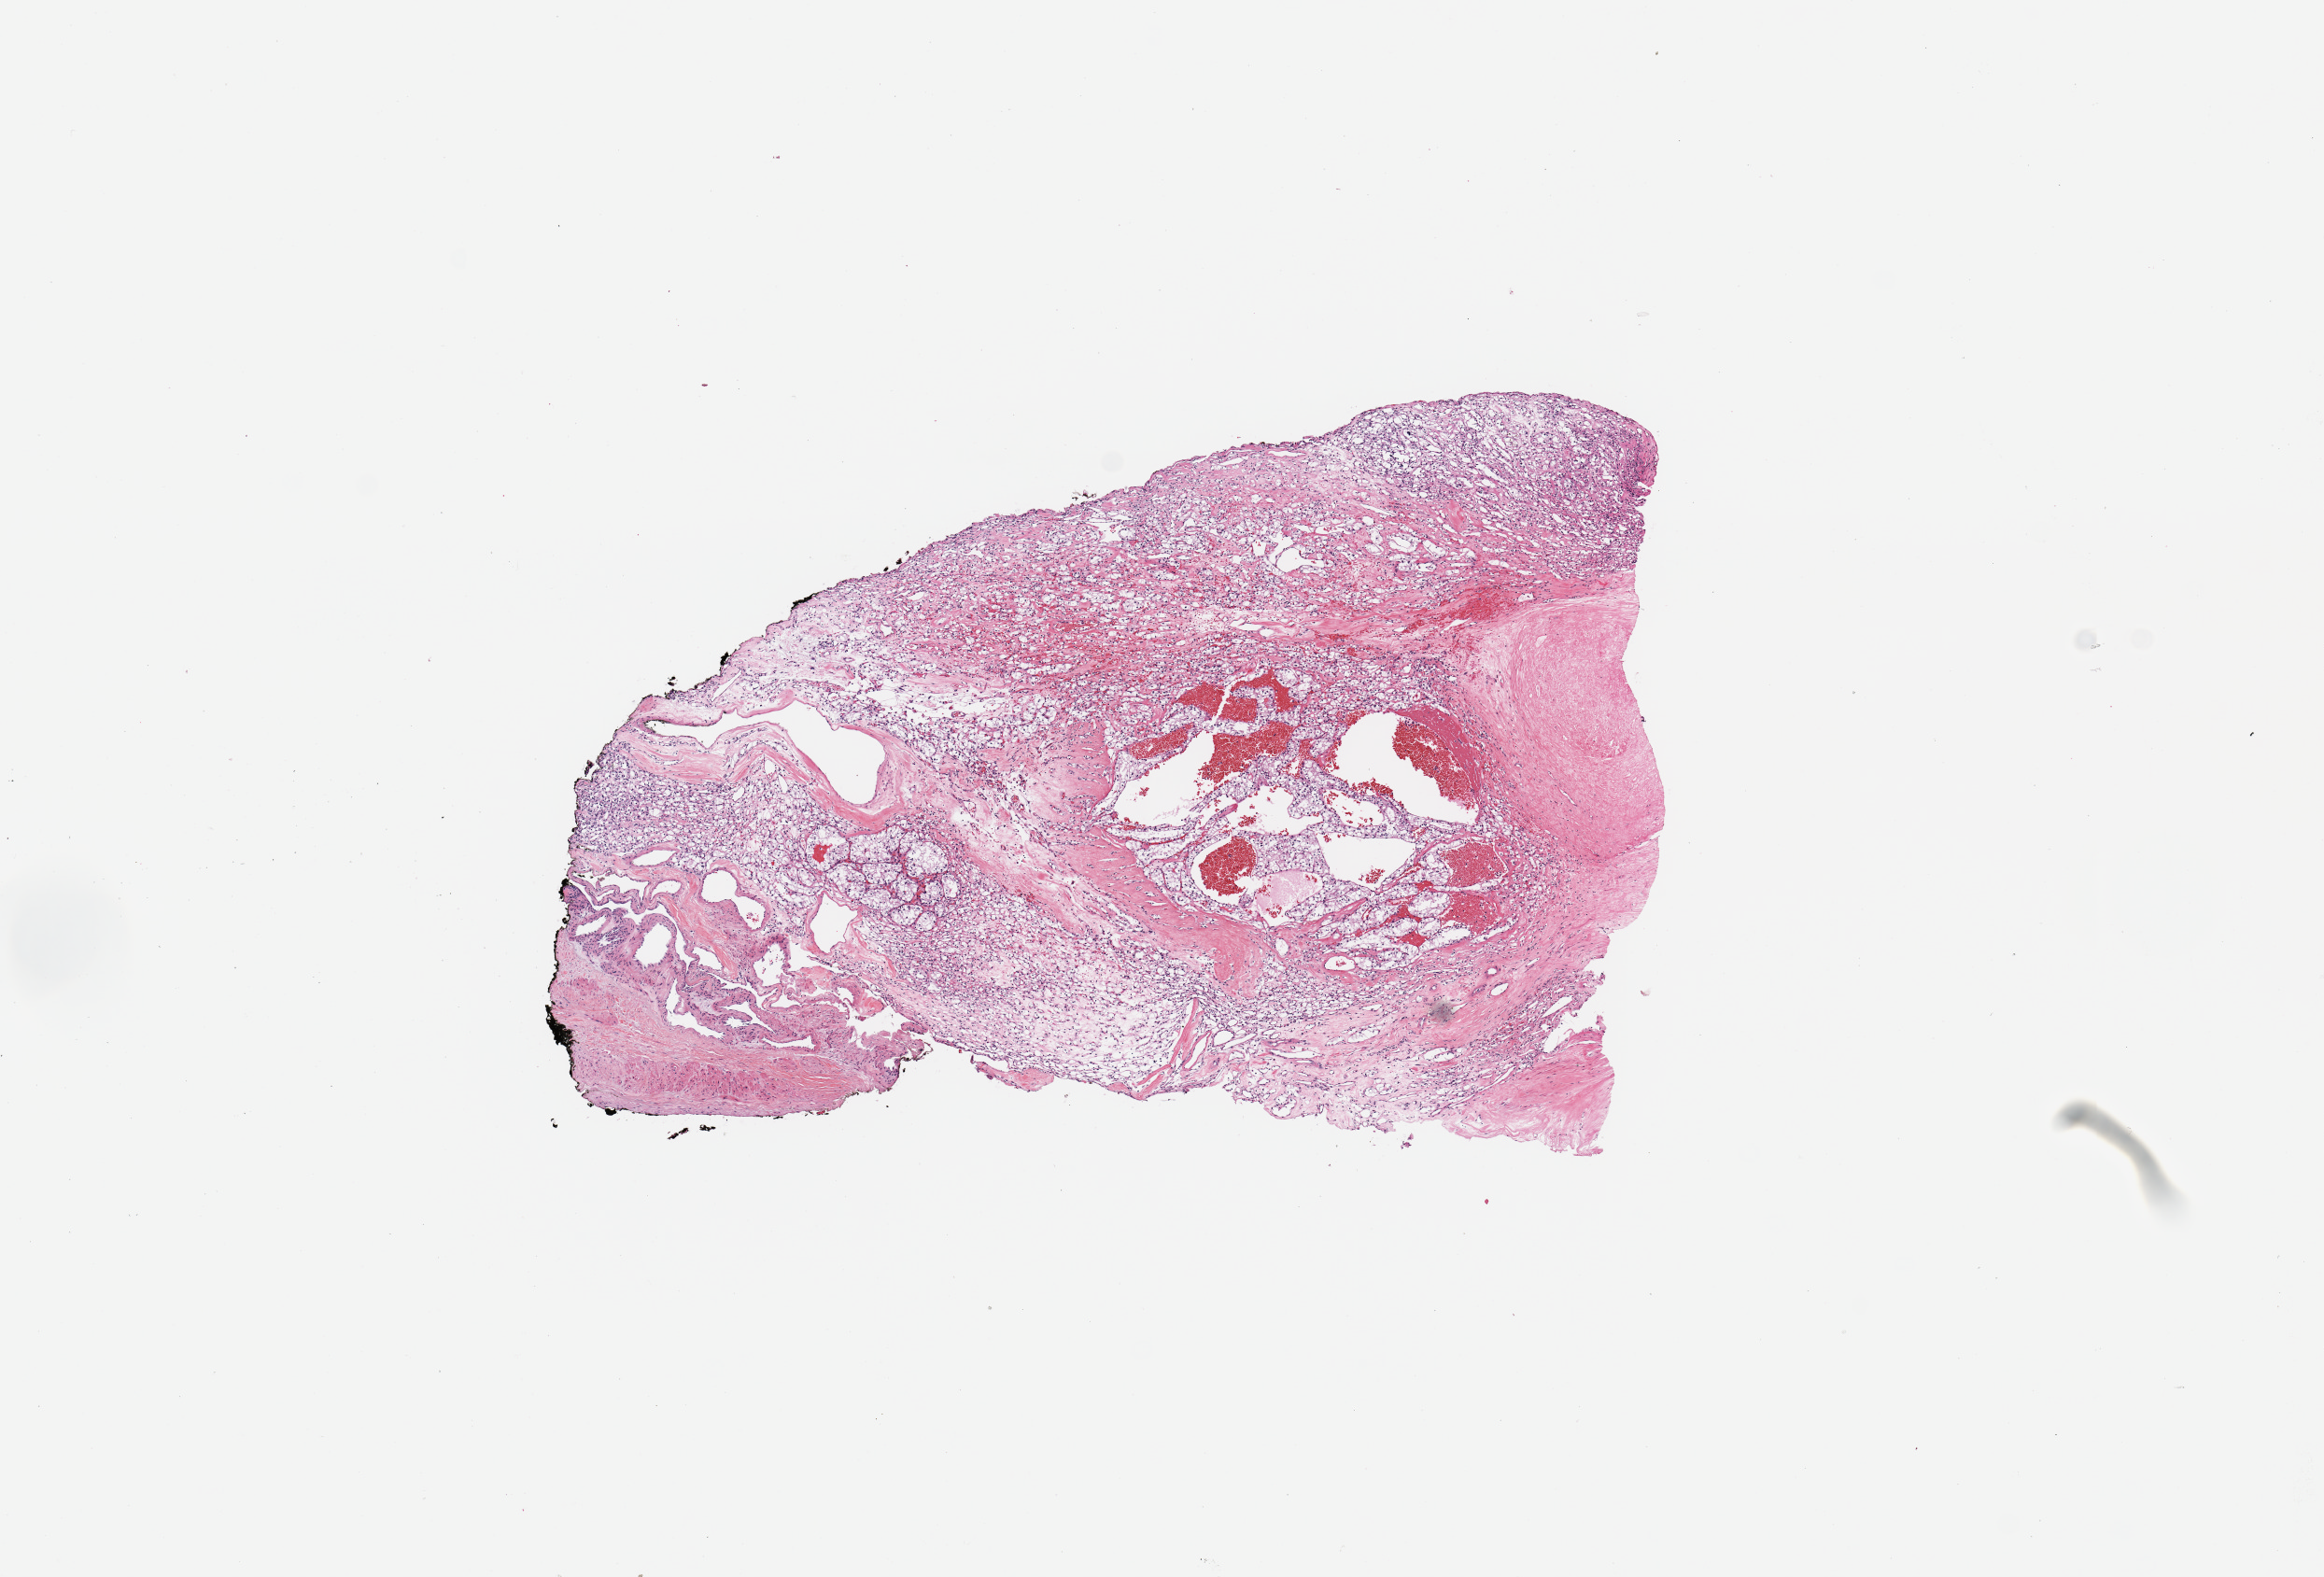
Whole-slide histology image, Hematoxylin and eosin (H&E) stained, a low-resolution overview of the entire scanned area, about 9.8 x 6.7 mm; tumour tissue sample, sampled site: kidney. Male, 47 y/o. Histologic grade: G3 (poorly differentiated). Slide review estimates, as recorded: tumour nuclei 80%, necrosis 0%.
Diagnosis: Renal cell carcinoma, NOS. AJCC pathologic stage: I.